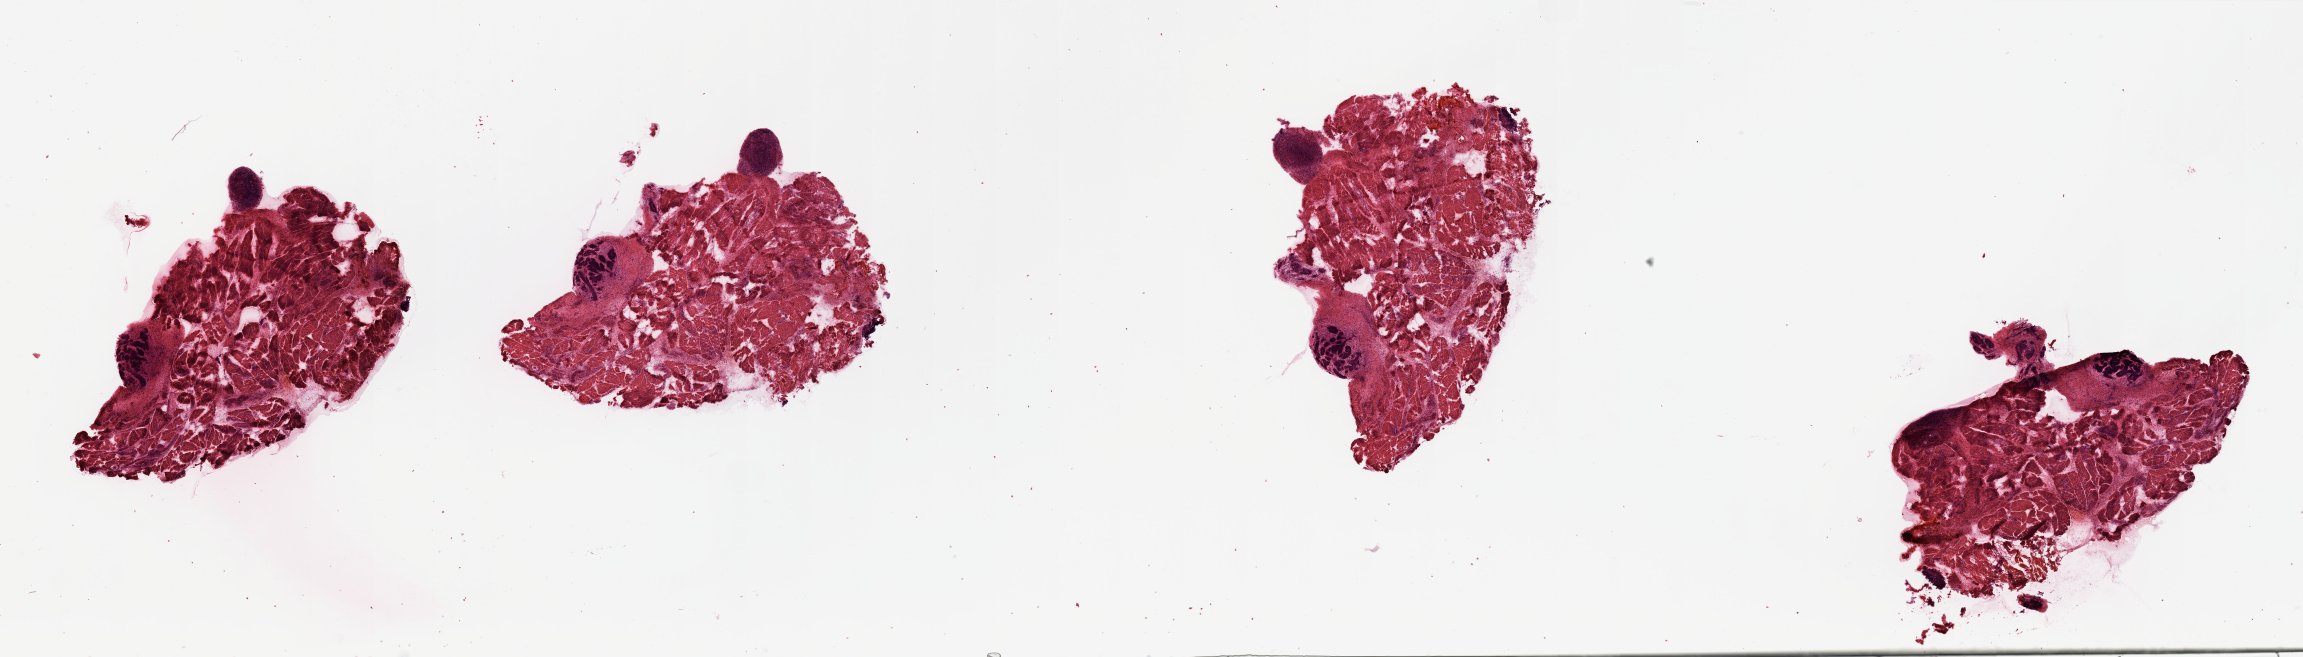
Digitized H&E tissue section (whole slide) — a low-resolution overview of the entire scanned area, about 36.4 x 10.4 mm (slide scanned at 20x), head and neck, tissue type not recorded. Male, 53 y/o.
Patient diagnosis: Squamous cell carcinoma, NOS.